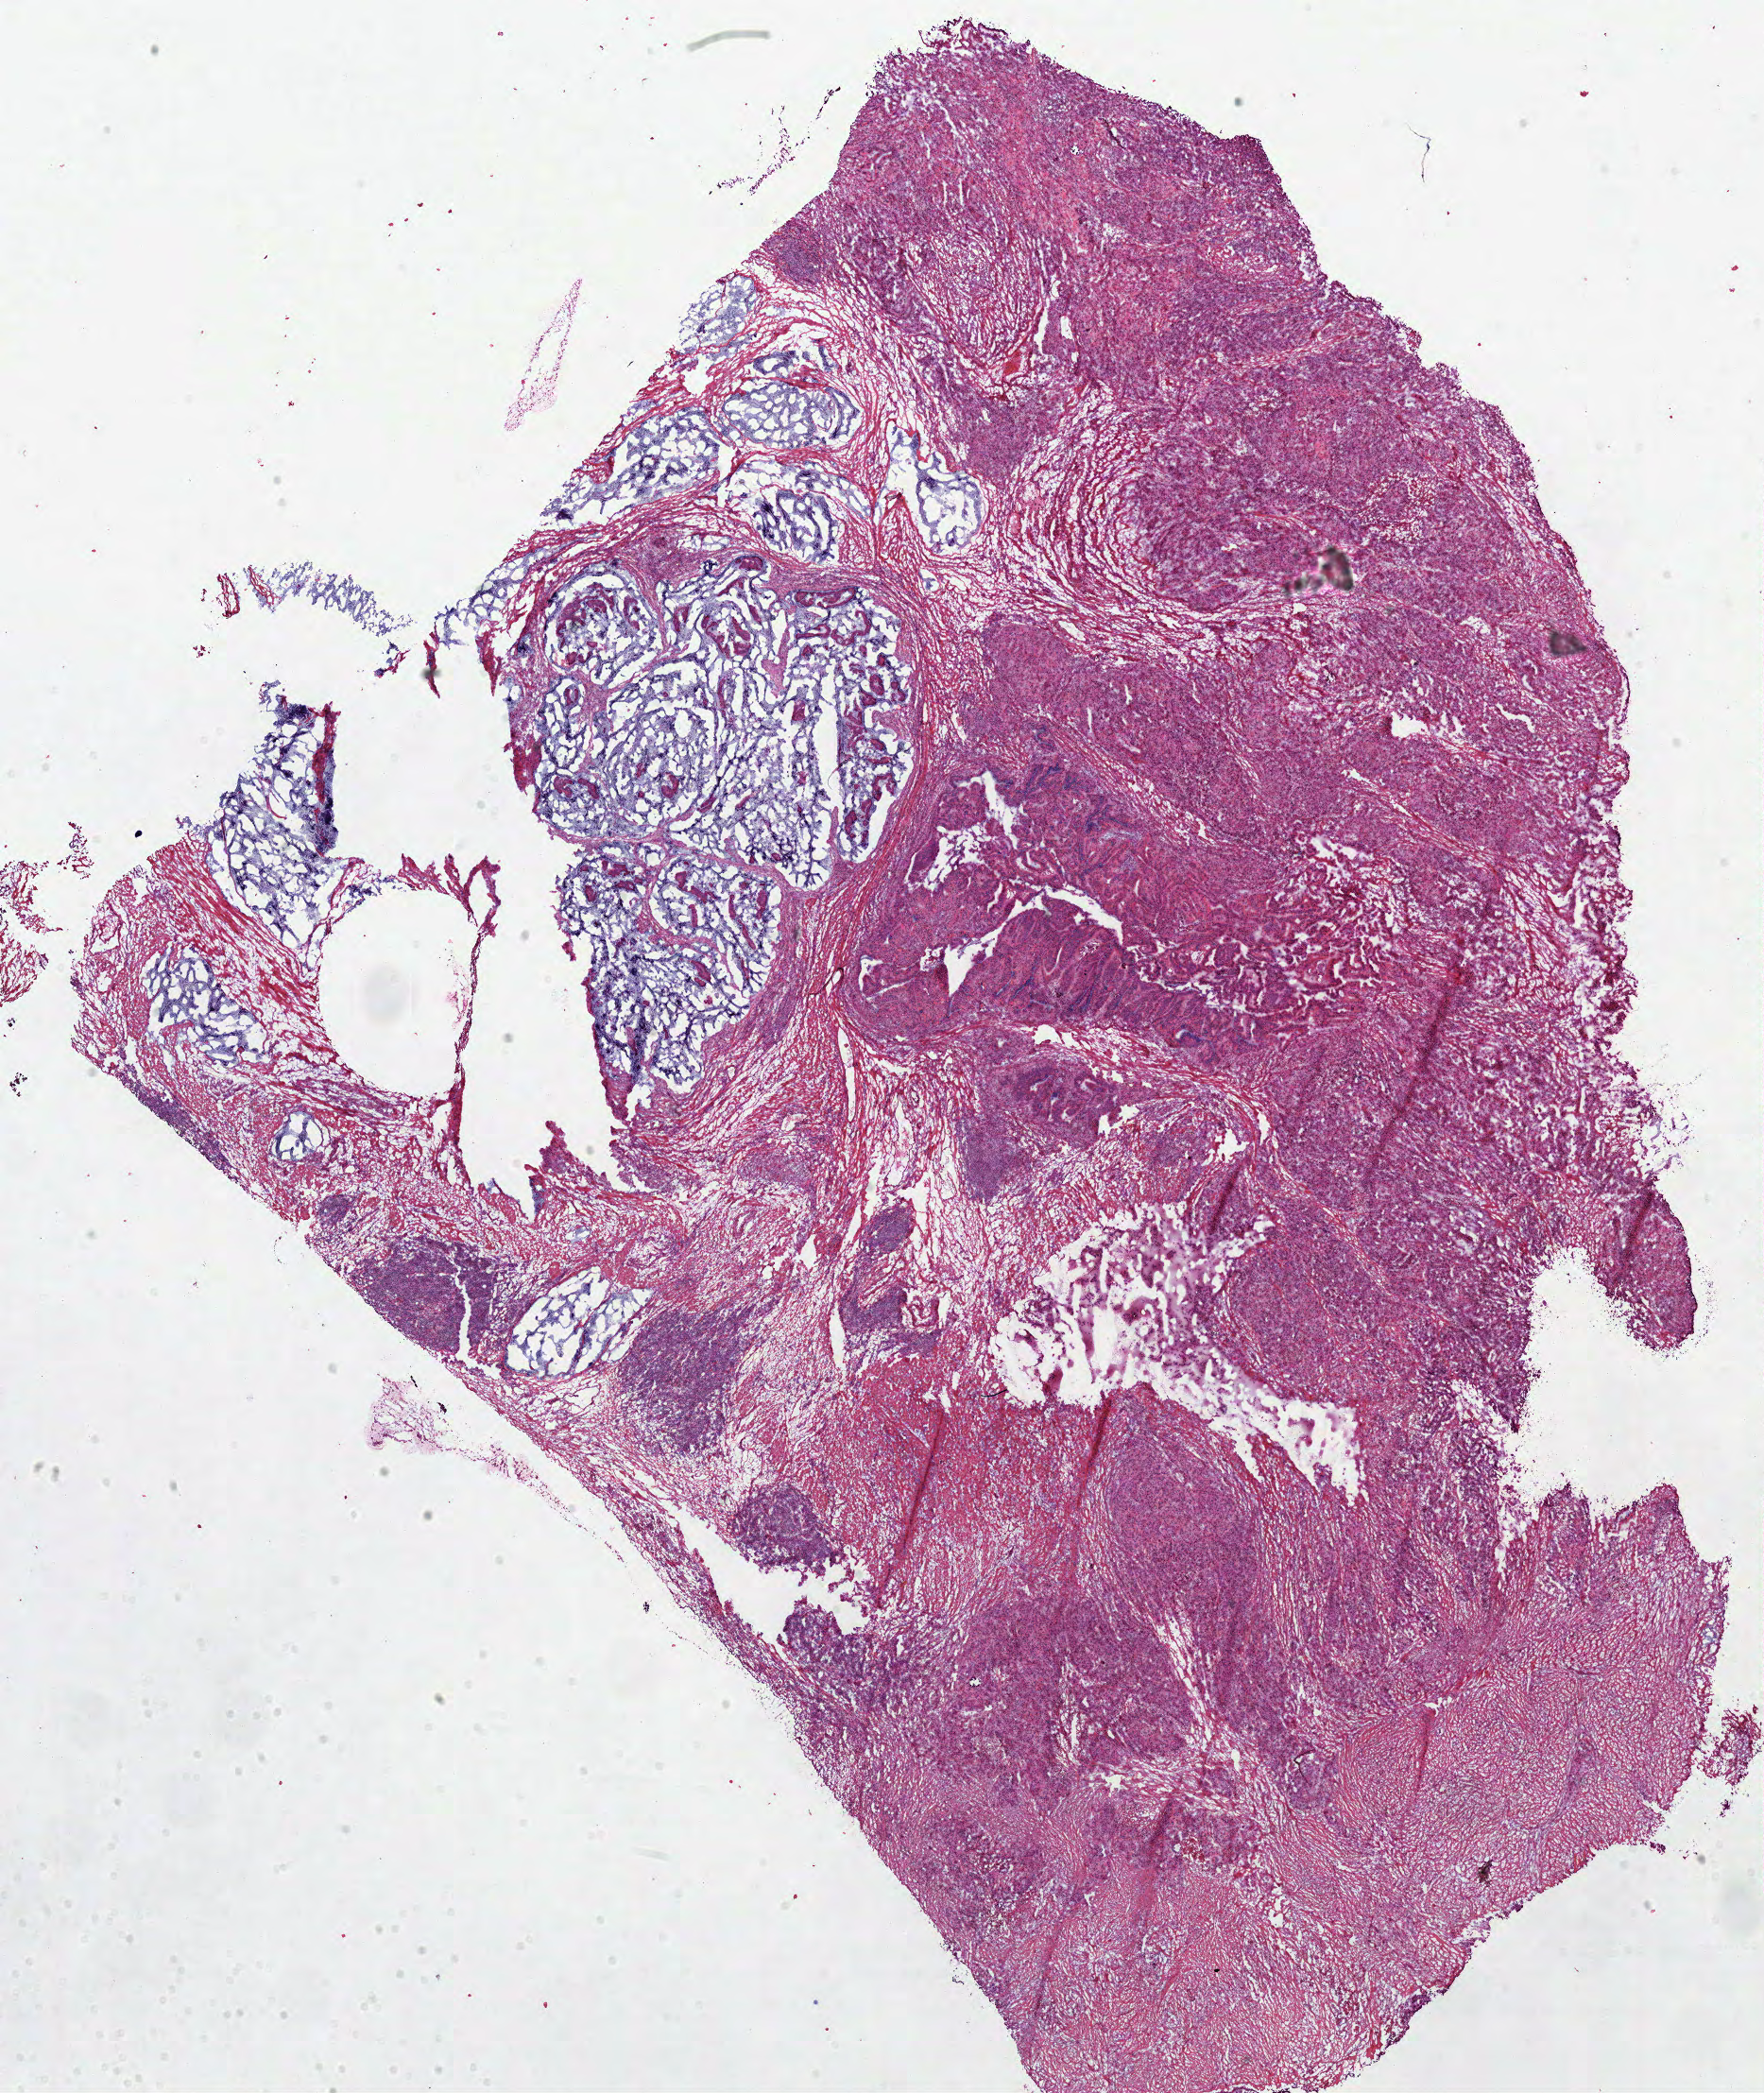
Whole-slide histology image, H&E — low-resolution overview of the scanned area, about 14.7 x 17.4 mm (from a 40x scan), frozen section from the top of the tissue portion, colon, primary tumour sample. Male, age 57 years at initial diagnosis. Slide review estimates, as recorded: tumour cells 78%, tumour nuclei 80%, normal cells 0%, stromal cells 20%, necrosis 2%.
AJCC pathologic stage: IIA. TNM: T3 N0 M0. Pathologic diagnosis: Mucinous adenocarcinoma.